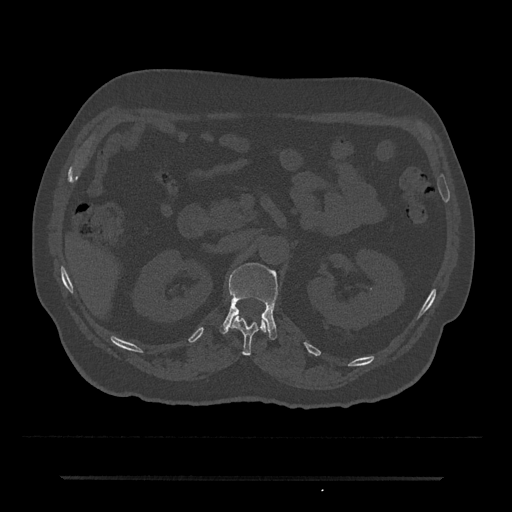
CT including the spine, one axial slice; reconstruction kernel Br40s/3; bone window (W 1800 / L 400 HU); 0.5 mm slice thickness; 512 × 512 image matrix. Patient: male, 69 years. From the clinical record (not read from this slice): primary cancer: prostate.
Annotated regions visible in this slice (semi-automatic segmentation, software-assisted and operator-edited):
- L1 vertebra: bounding box (x1, y1, x2, y2) in pixels: (219, 262, 278, 340)
- T12 vertebra: (231, 314, 268, 355)